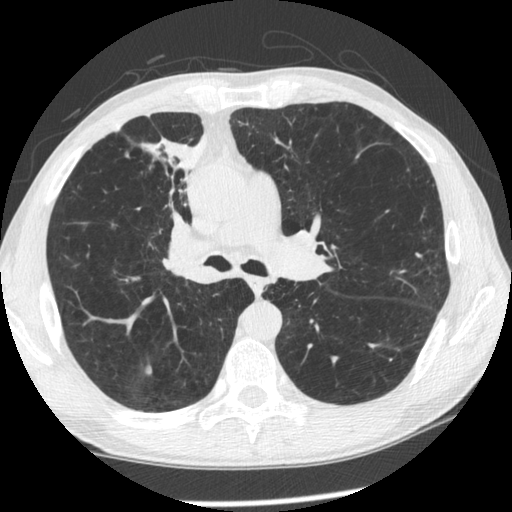
Low-dose screening chest CT, one axial slice; position 143 of 261 along the scan axis; reconstruction kernel STANDARD; lung window (W 1500 / L -600 HU); 1.25 mm slice thickness; 512 × 512 image matrix.
Structures marked on this image (outlined manually by an expert reader):
- lesion 1 (tumor, upper lobe of right lung): bounding box <142,134,207,236> (left, top, right, bottom; pixels)